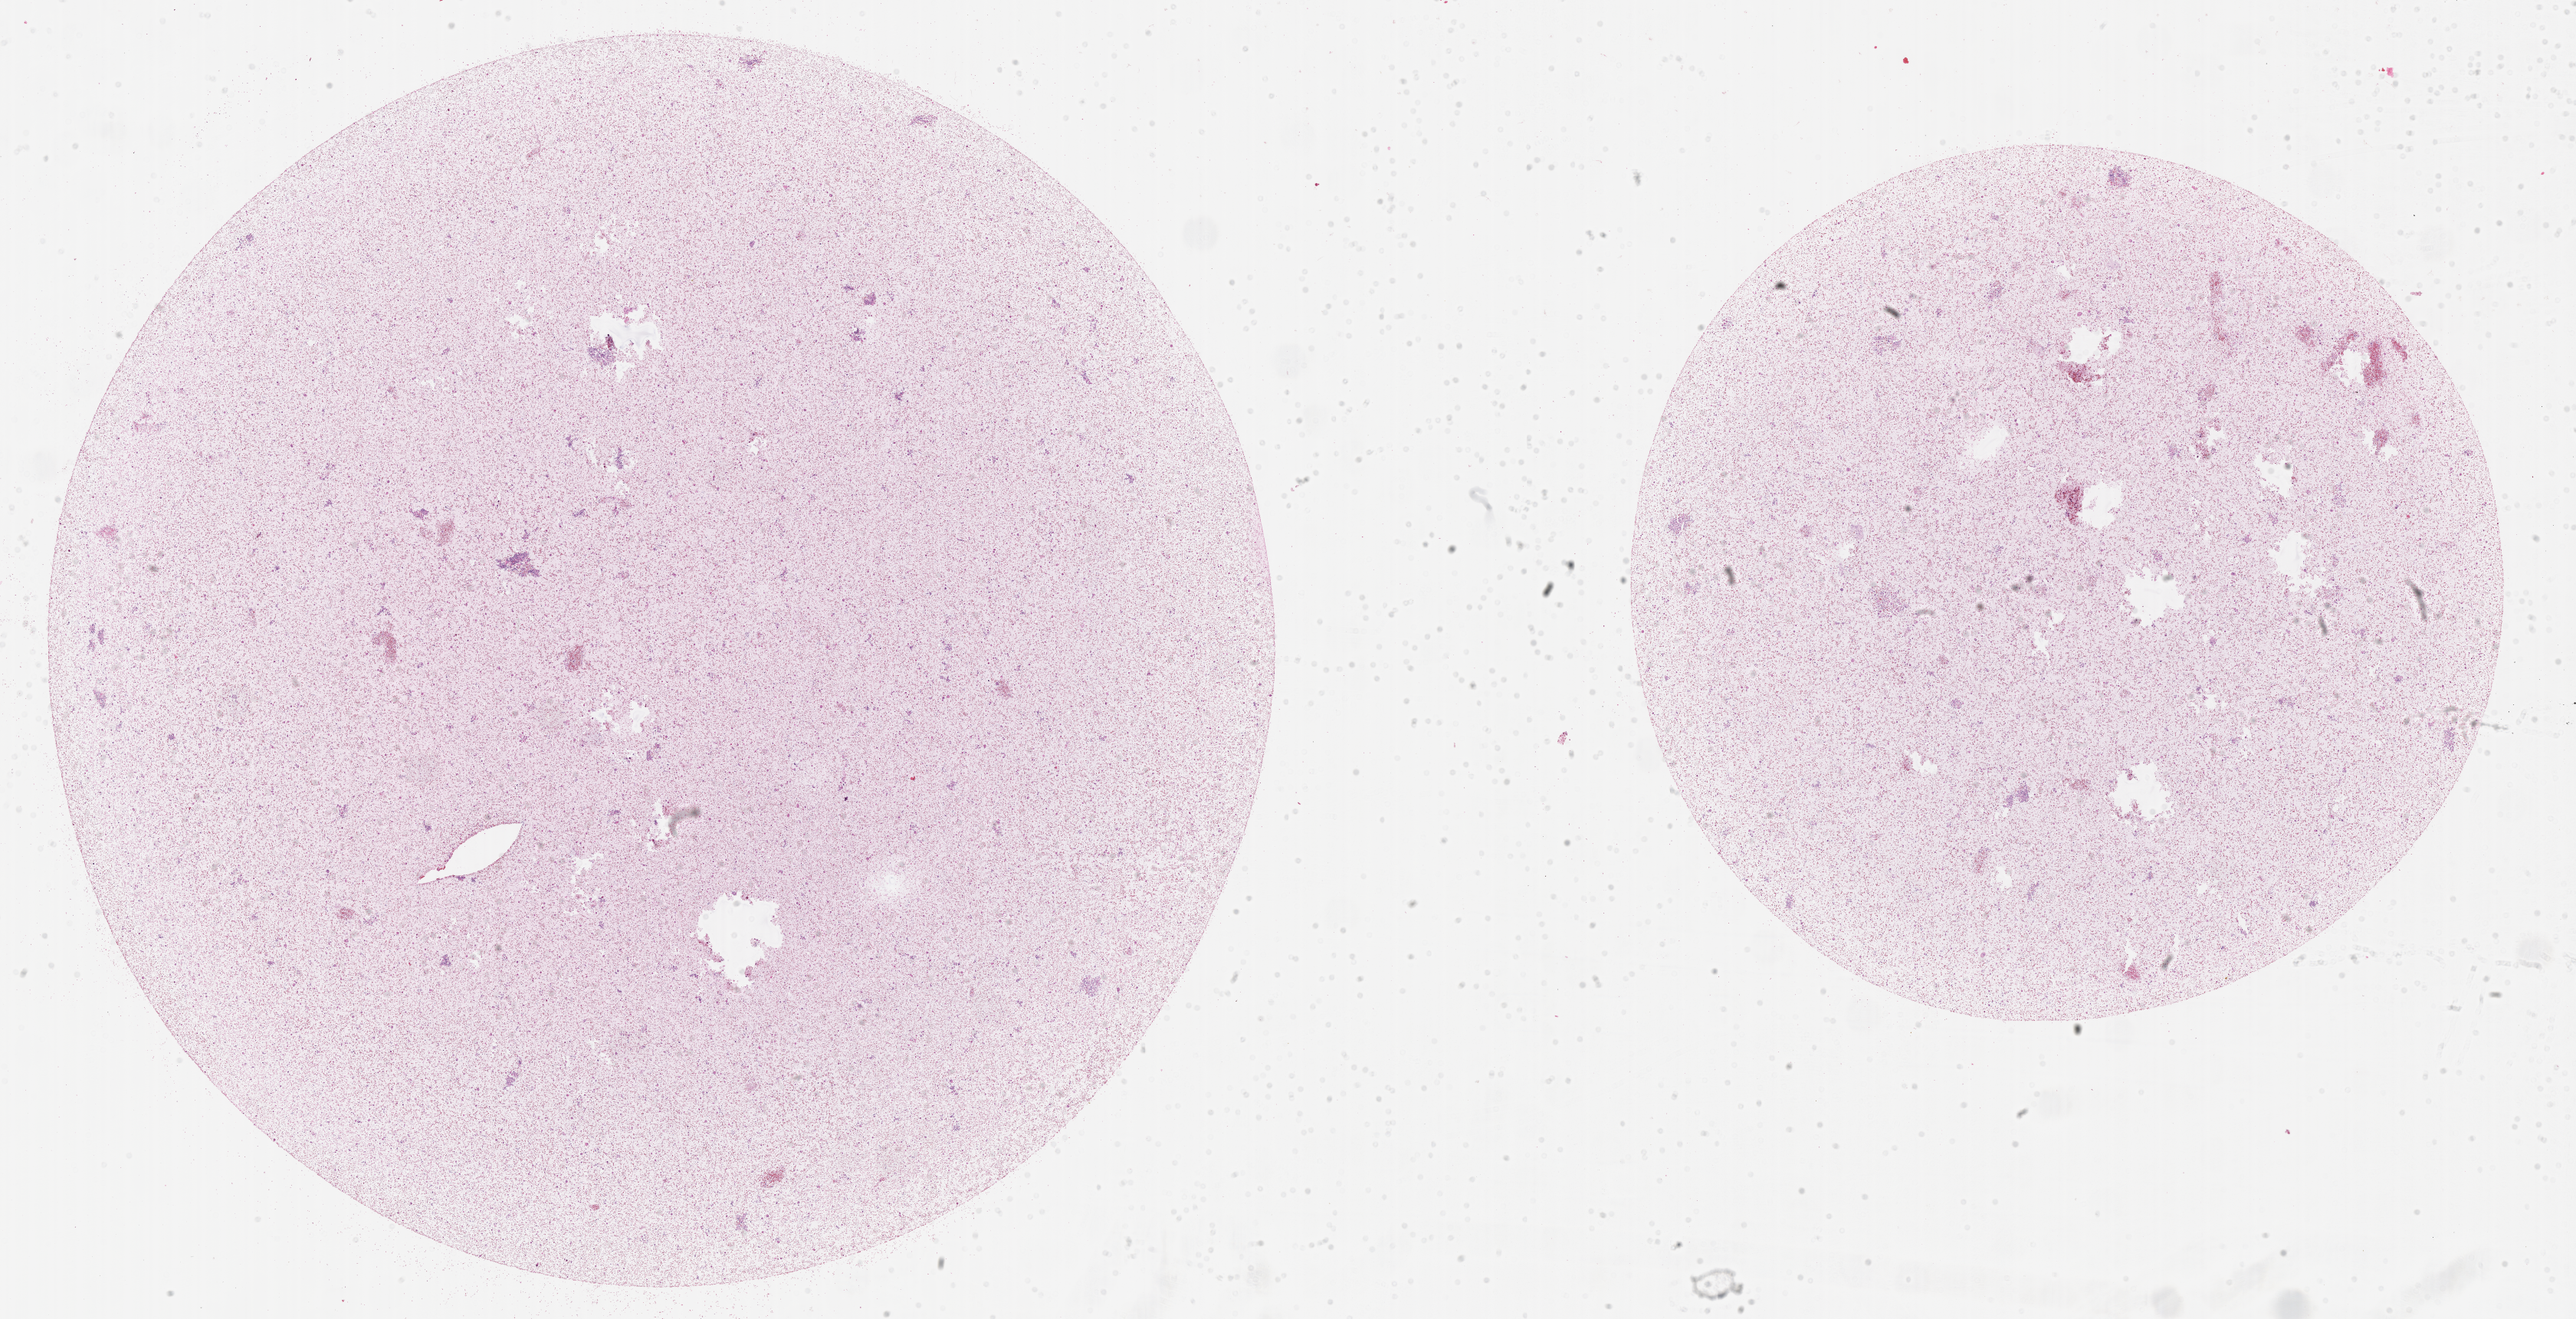
Whole-slide image, hematoxylin and eosin (H&E) stain of tumor tissue — whole scanned area (about 27.2 x 13.9 mm) shown as a low-resolution overview; FFPE section; site: soft tissue, pelvis. Female patient, age at diagnosis 11.6 years.
• metastatic status at presentation (as recorded): non-metastatic (unconfirmed)
• diagnosis: rhabdomyosarcoma; histological classification: rhabdomyosarcoma nos
• stage (as recorded): 3